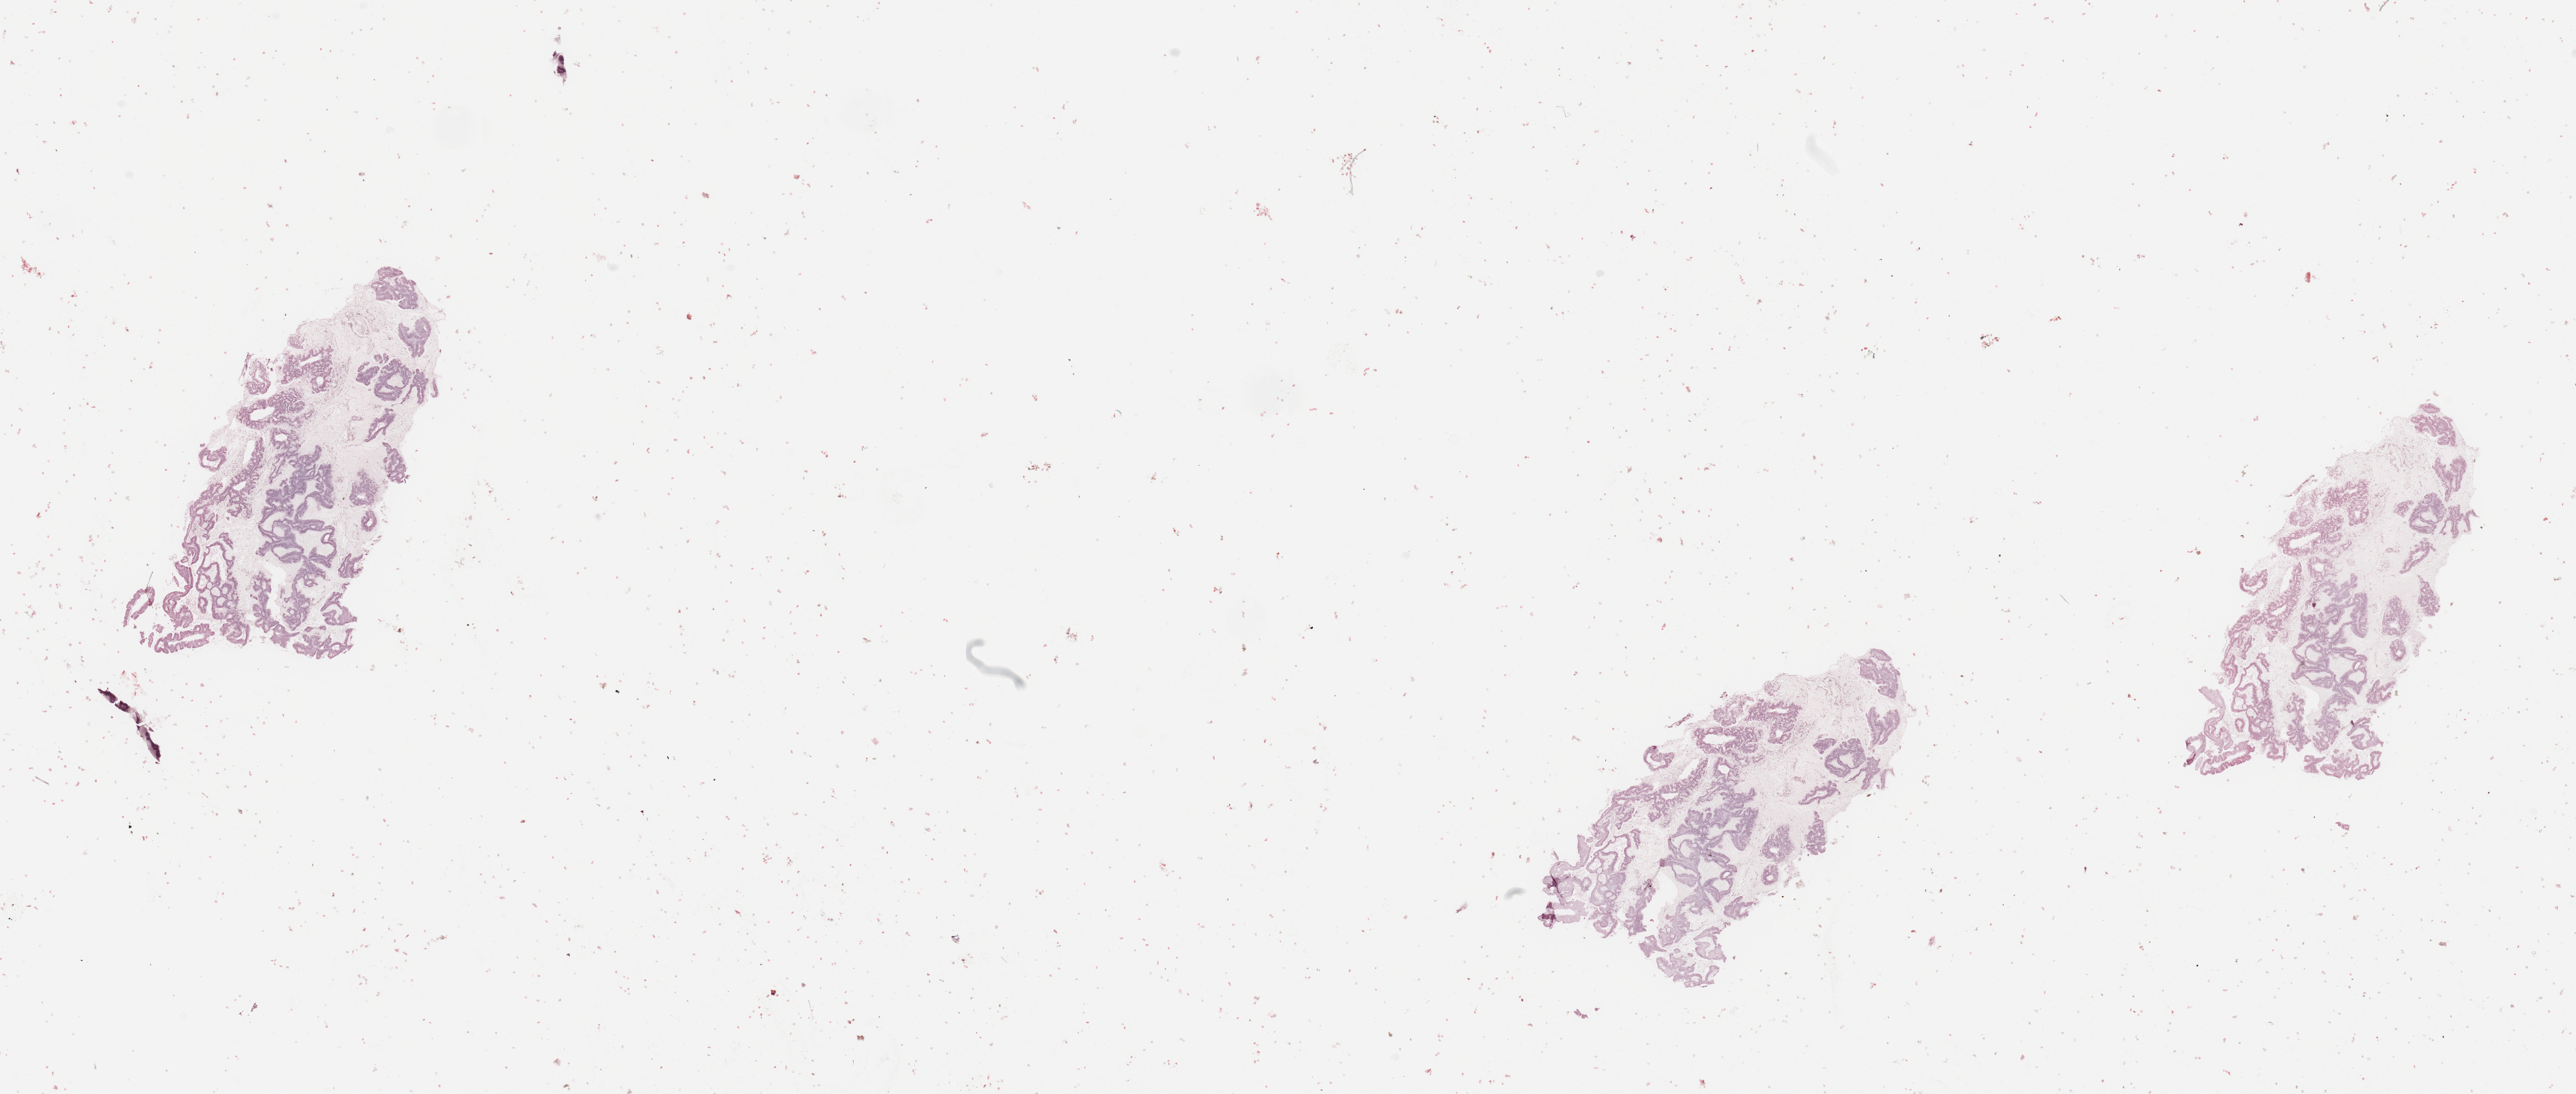
Hematoxylin and eosin (H&E) stained whole-slide image — a low-resolution overview of the entire scanned area, about 31.5 x 13.4 mm. Tumour tissue sample, sampled site: uterus. Patient: female, age 66 years. Histologic grade: G2 (moderately differentiated). Slide review estimates, as recorded: tumour nuclei 90%, necrosis 0%.
- histologic diagnosis: Endometrioid adenocarcinoma, NOS
- AJCC pathologic stage: I
- primary tumour site (as recorded): posterior endometrium